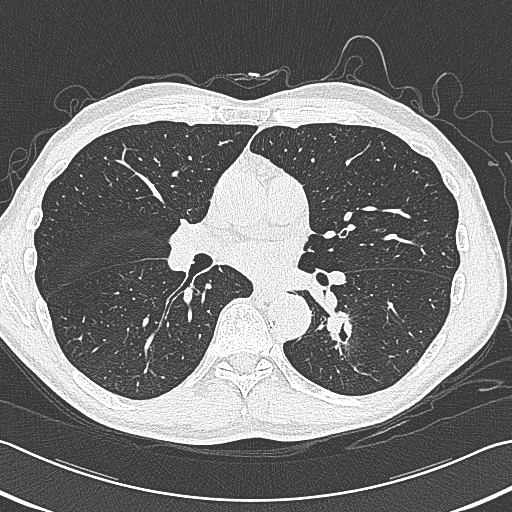
Axial slice from a low-dose chest CT screening exam, baseline annual screen, lung window (W 1500 / L -600 HU), 1 mm slice thickness, 512 × 512 image matrix, field of view 346 × 346 mm. Male participant, aged 59 years at enrolment. Former smoker at enrolment.
Lesion marked by an expert reader, bounding box [x1, y1, x2, y2] px = [313, 294, 375, 353]. Reader record for this screening exam (exam-level; its link to the box is not recorded): non-calcified nodule or mass ≥4 mm, left lower lobe, 15 × 15 mm, smooth margins, soft tissue attenuation. Participant outcome: lung cancer diagnosed 17 days after this screen — squamous cell carcinoma, large cell, nonkeratinizing, NOS, left lower lobe, poorly differentiated (G3), stage IB (AJCC 6th edition), 31 mm at pathology.